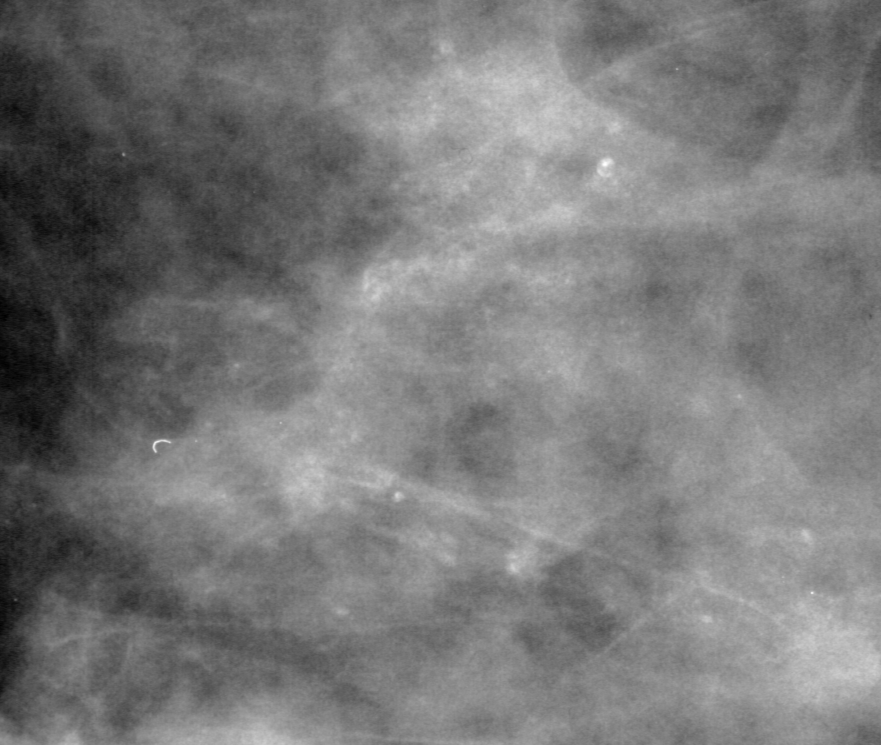
Cropped region of a digitized screen-film mammogram centred on a radiologist-marked abnormality; right breast; MLO view.
Calcifications, morphology pleomorphic, distribution segmental; BI-RADS assessment category 4; pathology (as recorded): benign.